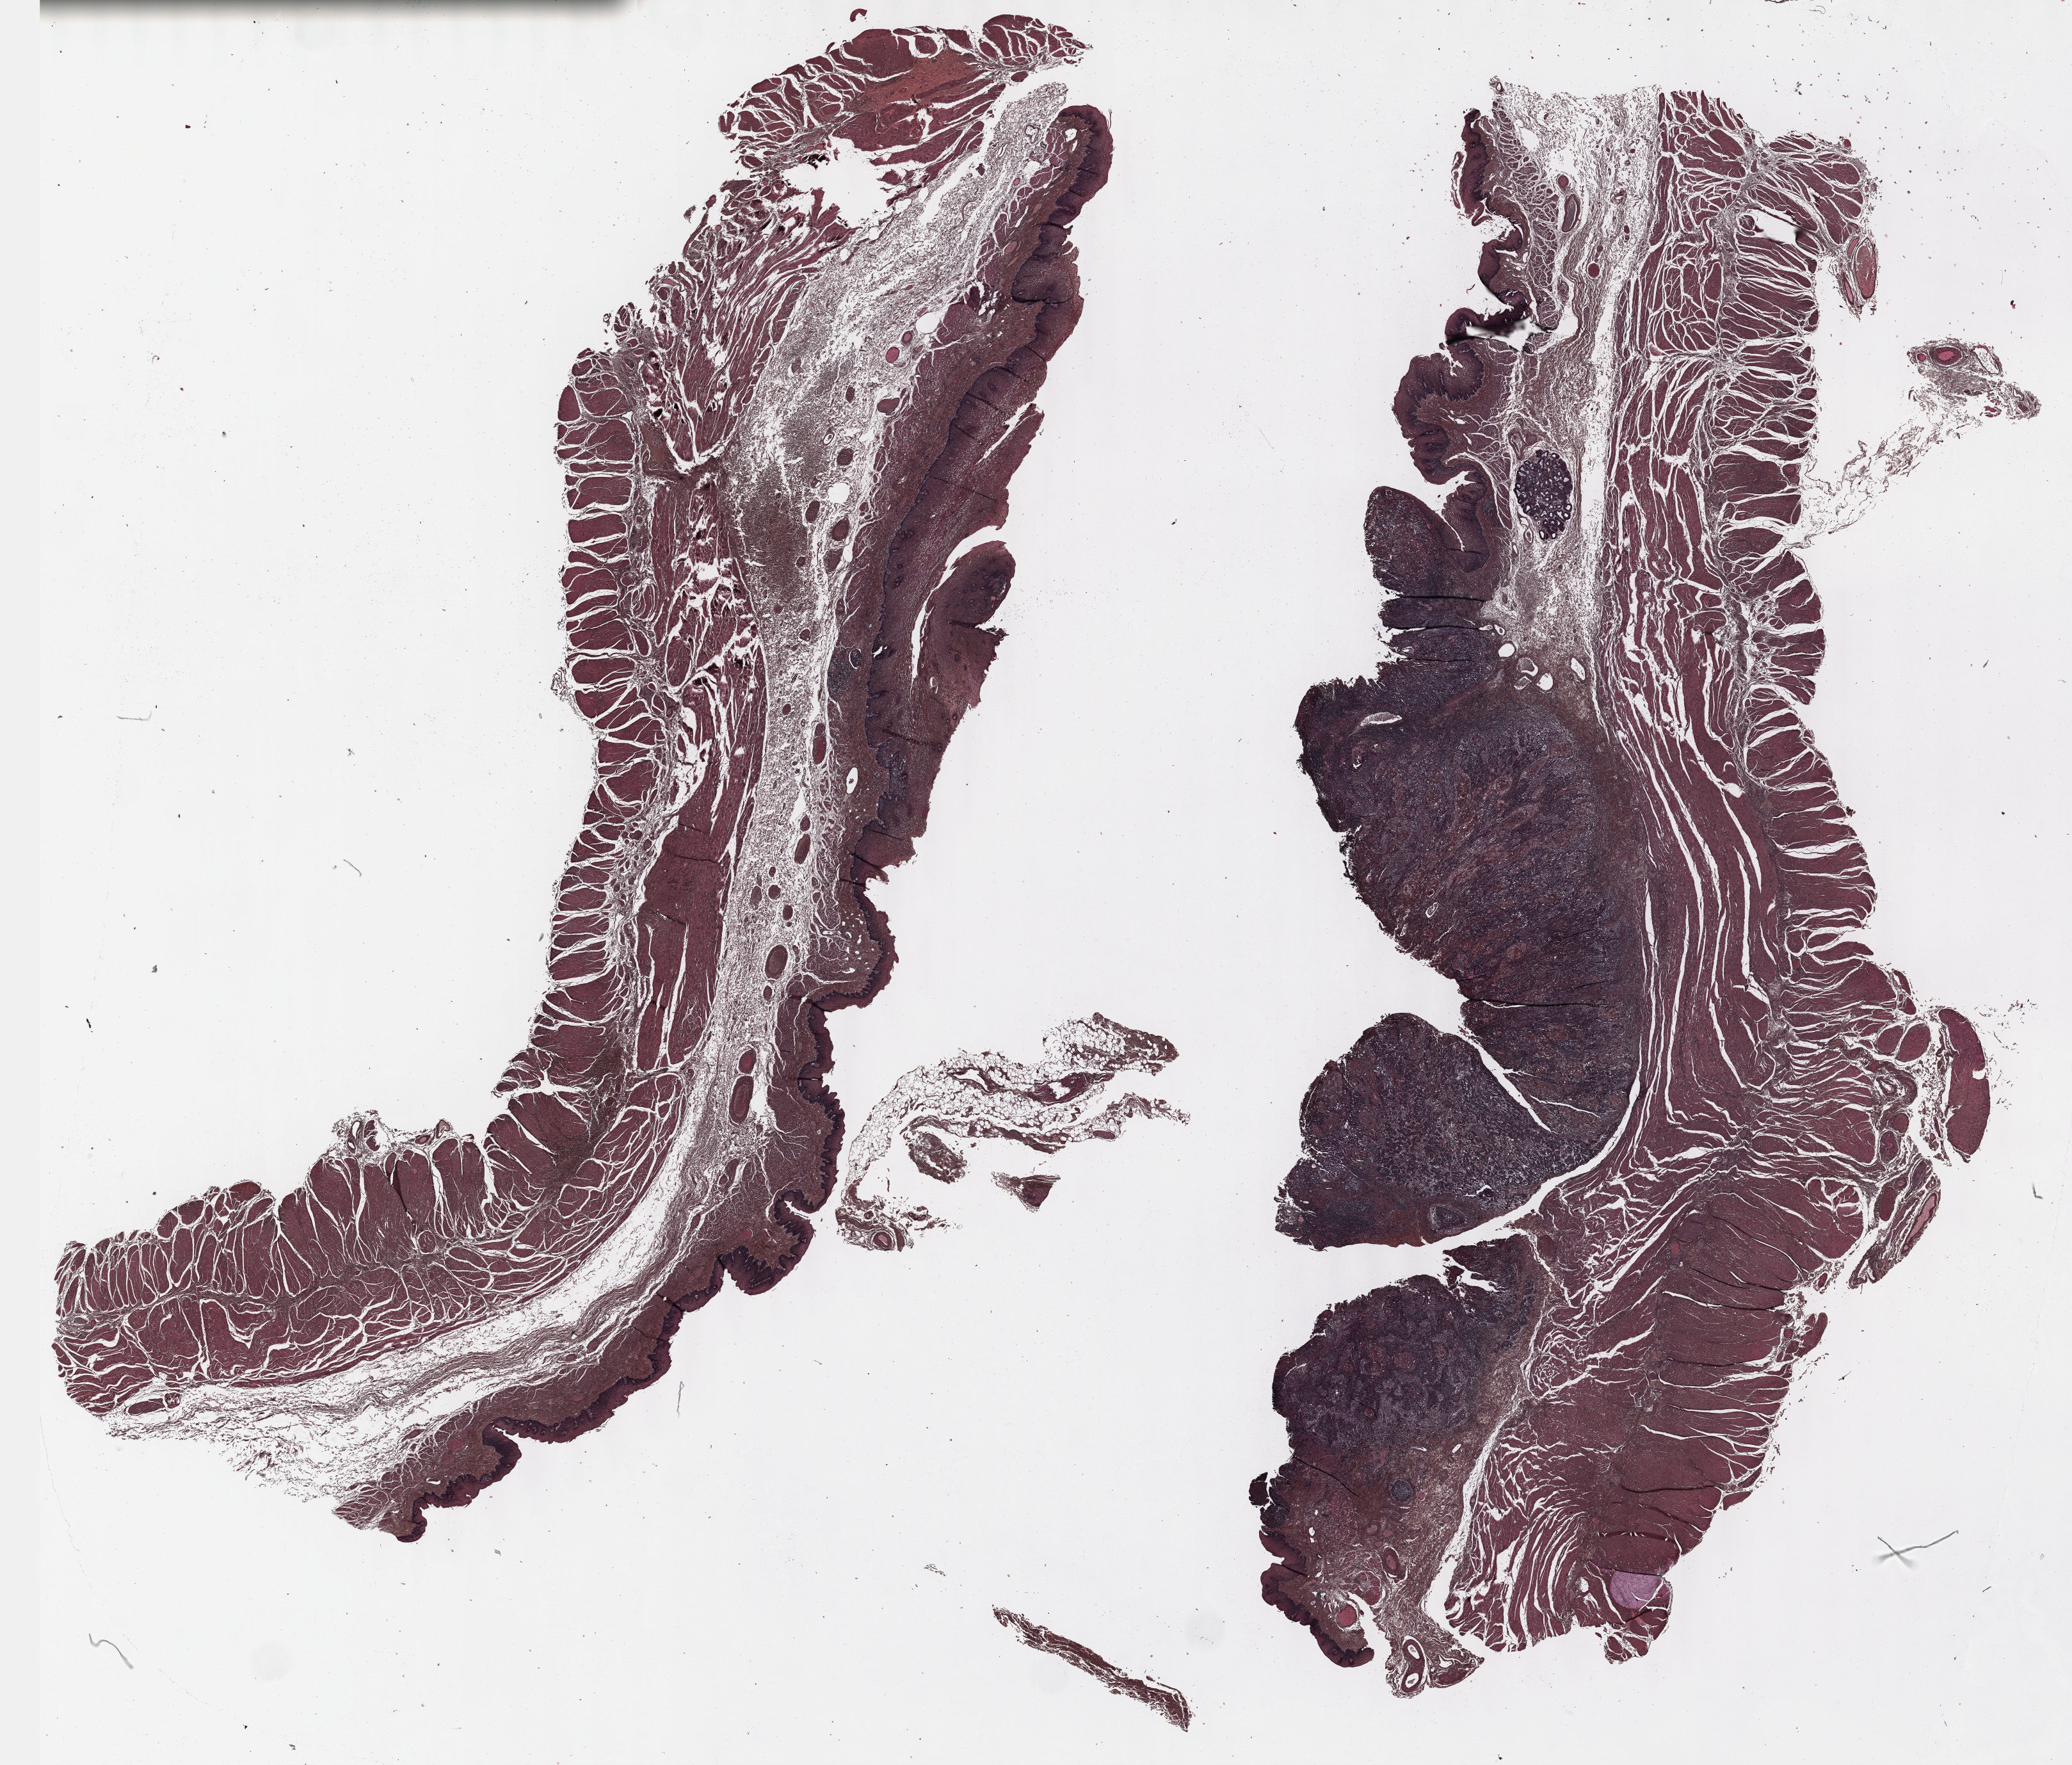
Whole-slide histology image, H&E, whole scanned area (about 26.2 x 22.3 mm) shown as a low-resolution overview, formalin-fixed paraffin-embedded (FFPE) diagnostic section, primary tumour sample from the esophagus. Male patient; age at initial diagnosis 51 years. Histologic grade: G2 (moderately differentiated).
* AJCC pathologic stage: IV (7th edition)
* histologic diagnosis: Squamous cell carcinoma, NOS (middle third of esophagus)
* TNM: T1 N1 M1